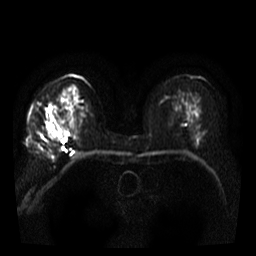
Breast MRI, one axial slice. Slice 20 of 40 in the series (ordered by position). Diffusion-weighted series; image 2 of 4 stored at this slice position (different b-values; order by instance number). 3 T. 5 mm slice thickness. 256 × 256 image matrix, field of view 300 × 300 mm. Female patient.
Annotated regions visible in this slice (expert manual segmentation):
- tumour on diffusion-weighted imaging: bounding box <45,129,58,144> (left, top, right, bottom; pixels)